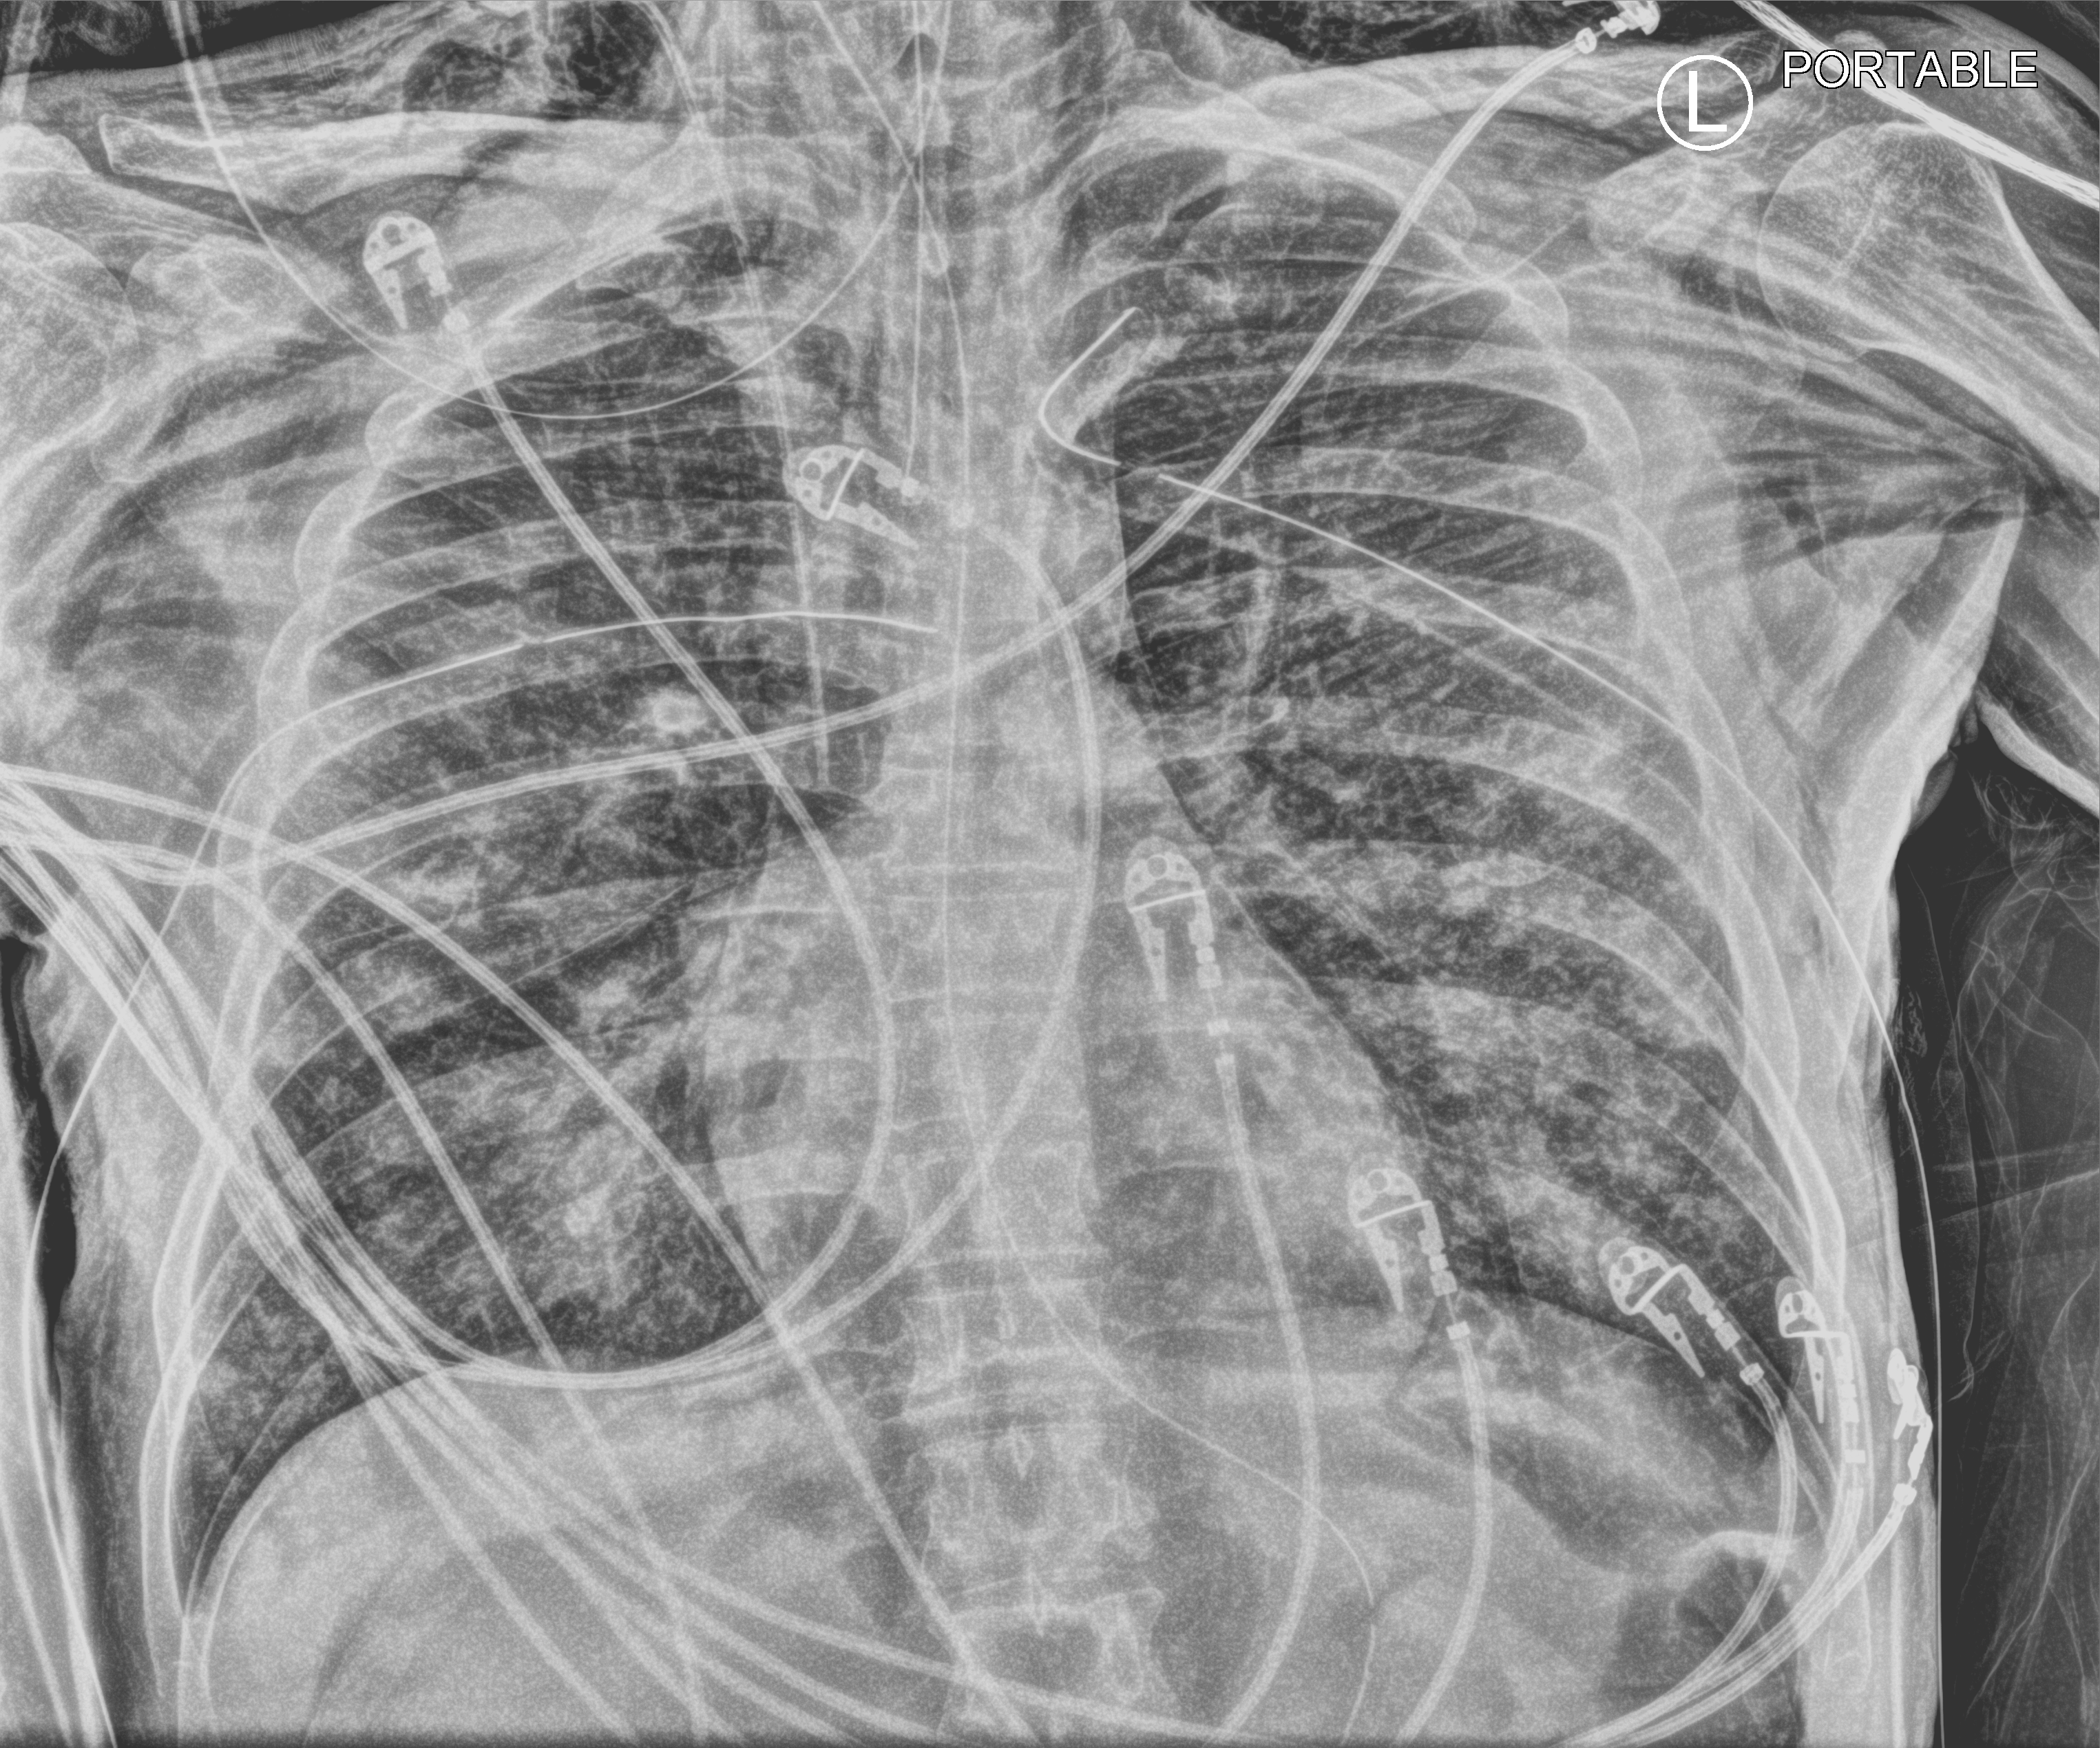
Portable chest radiograph. Patient hospitalised with COVID-19; male, aged 18–59 years.
From the hospital-stay record, not from the radiograph (when in the stay this image was taken is not recorded):
- mechanically ventilated during this hospital stay: yes
- admitted to intensive care during this hospital stay: yes
- diabetes (admission record): yes